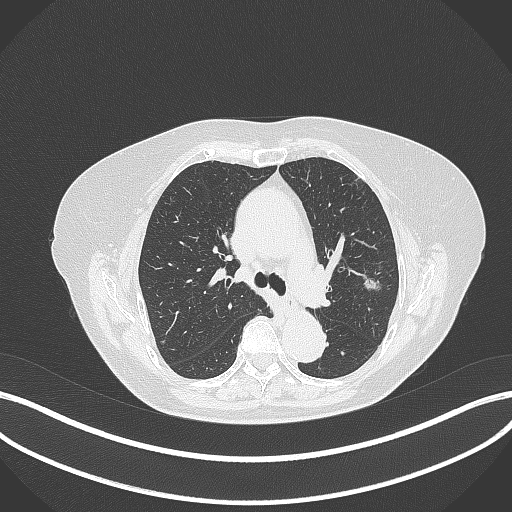
Chest CT, one axial slice; reconstruction kernel B70f; lung window (W 1500 / L -600 HU); 512 × 512 image matrix, field of view 400 × 400 mm. Female patient, age 75 years. From the clinical record (not read from this slice): clinical TNM (as recorded): T1c N0 M0.
Annotated regions visible in this slice (rectangle marked by the reading radiologist):
- lung tumour (recorded histology: adenocarcinoma): bounding box (x1, y1, x2, y2) in pixels: (363, 273, 383, 293)